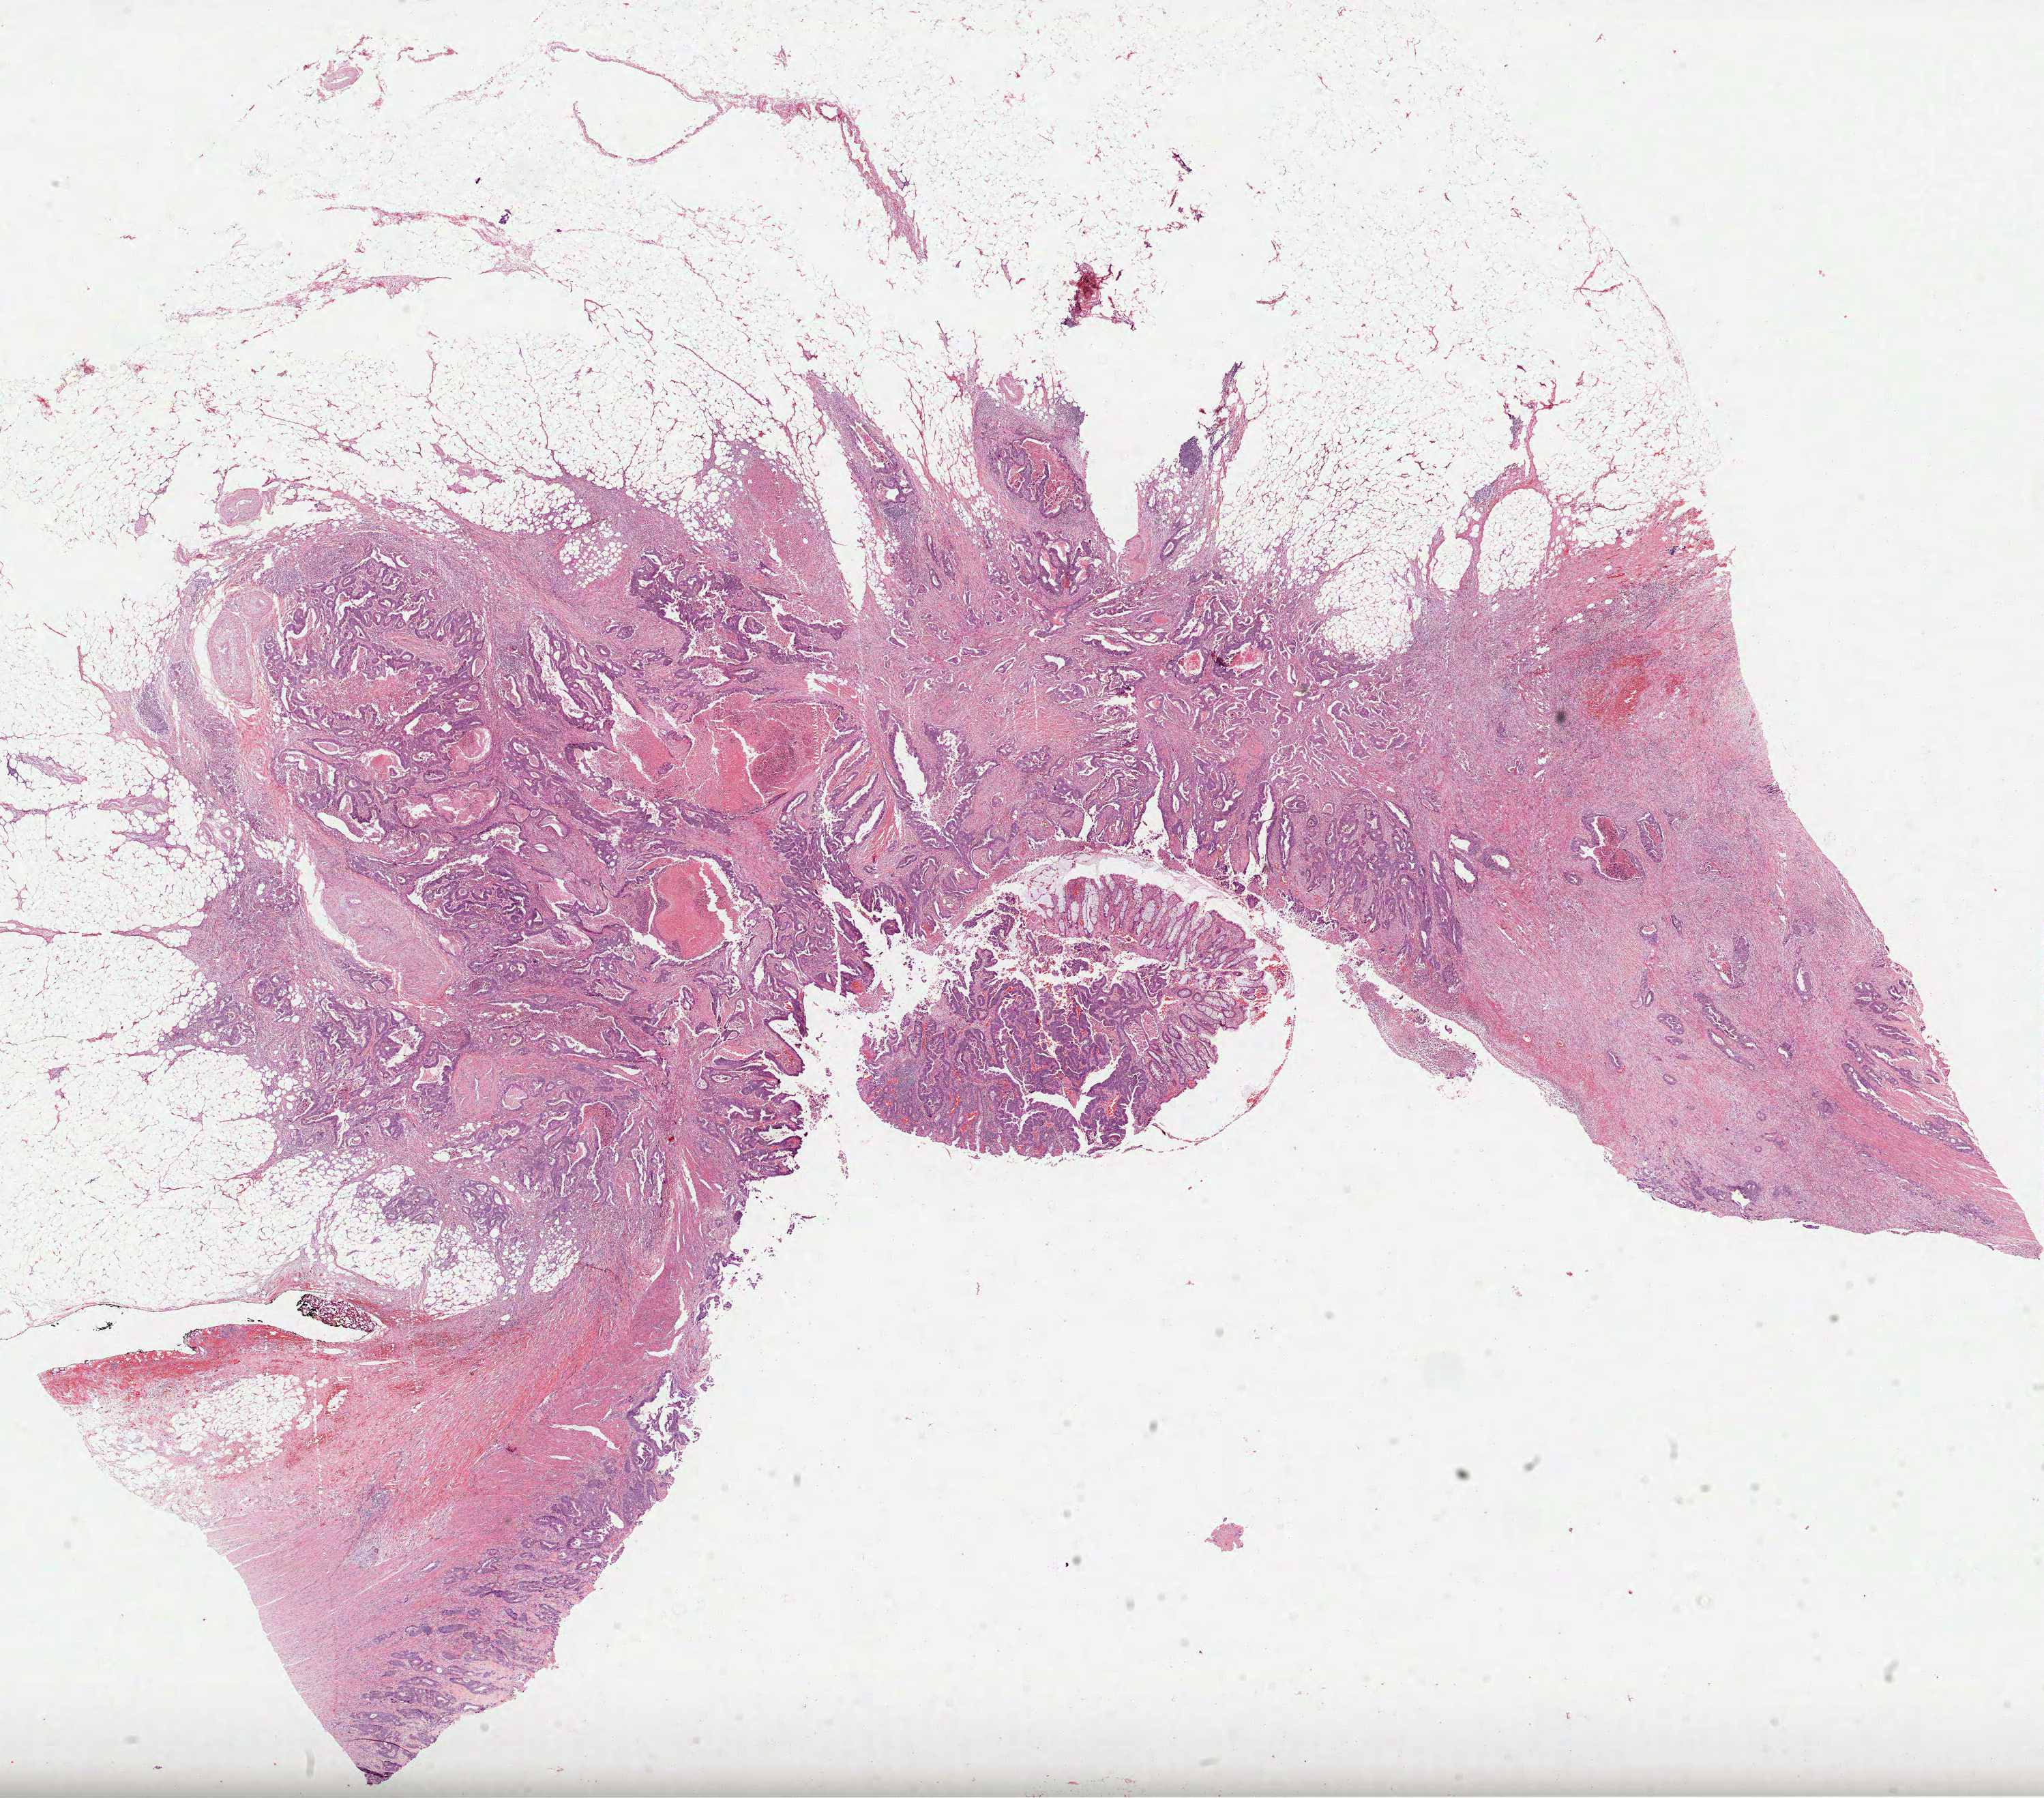
H&E-stained whole-slide image — shown as a low-resolution overview of the whole scanned area (about 24.2 x 21.3 mm, slide scanned at 40x), formalin-fixed paraffin-embedded (FFPE) diagnostic section, primary tumour sample from the rectum. Male patient; age at initial diagnosis 72 years.
Histologic diagnosis: Adenocarcinoma, NOS (rectosigmoid junction).